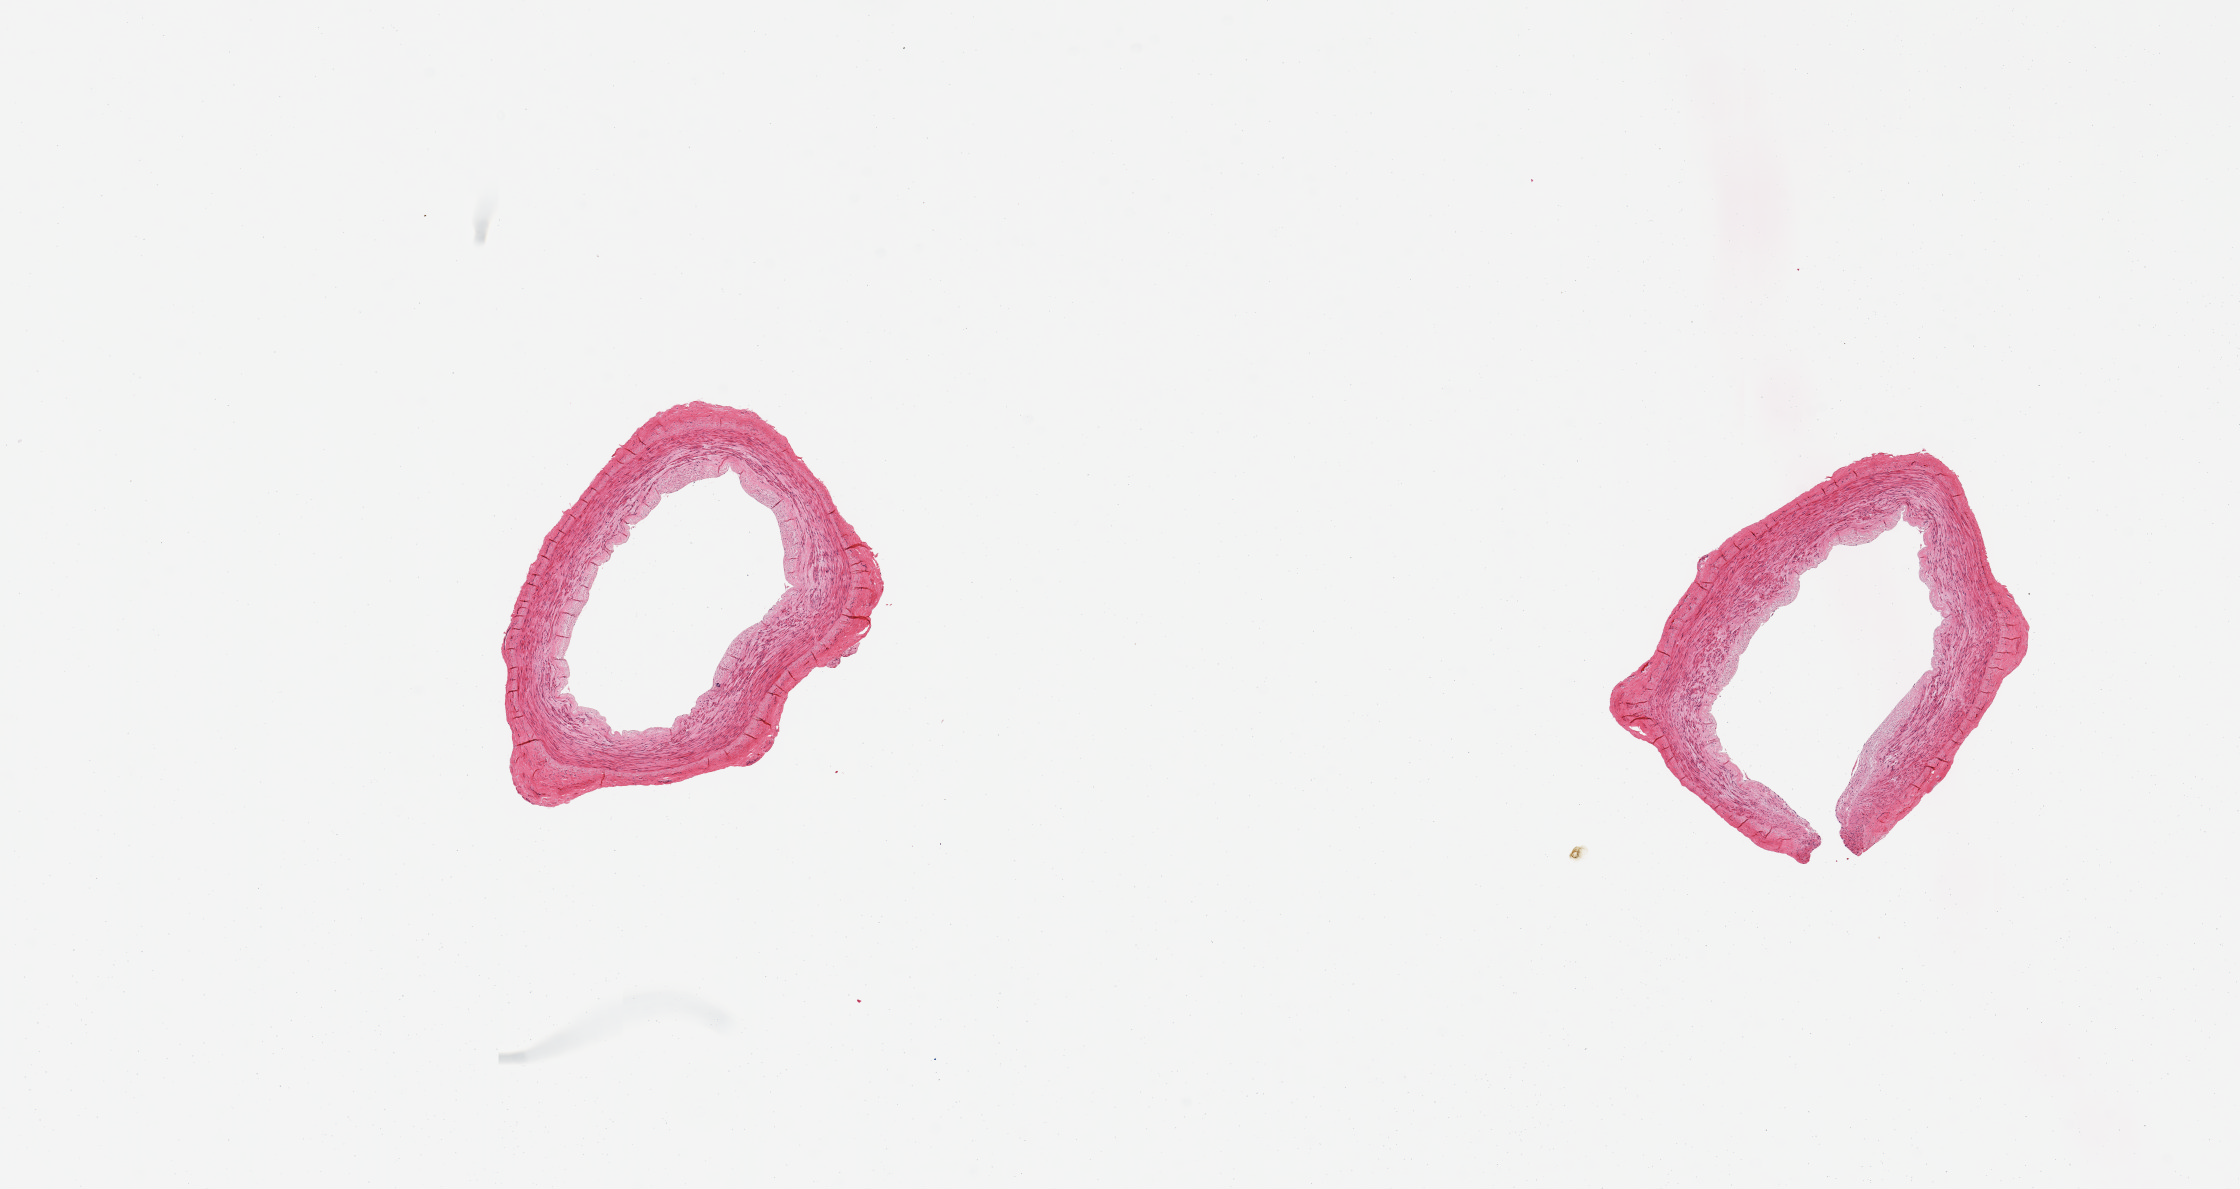
Digitized H&E-stained section, whole scanned area (about 17.7 x 9.4 mm, slide scanned at 20x) shown as a low-resolution overview, PAXgene-fixed paraffin-embedded (PFPE) section, section of tibial artery (target tissue), donor tissue sample. Donor: male.
• review note (as recorded): 1 piece; artery NOT nerve; no plaque; well trimmed